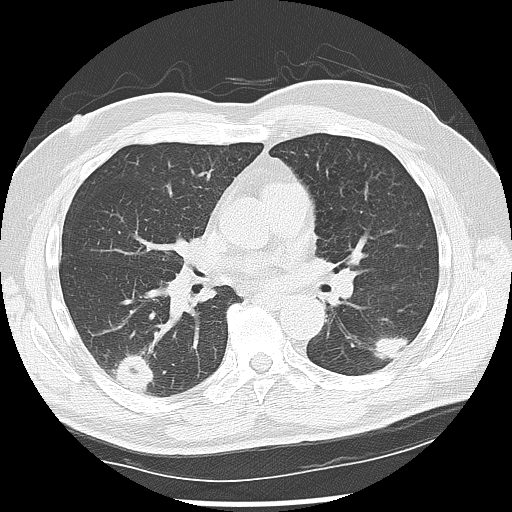
Low-dose screening chest CT, one axial slice; position 69 of 142 along the scan axis; reconstruction kernel LUNG; 120 kVp; lung window (W 1500 / L -600 HU); 2.5 mm slice thickness; 512 × 512 image matrix, field of view 360 × 360 mm.
Outlined on this slice (expert manual segmentation):
- lesion 1 (nodule, lower lobe of left lung): bounding box [x1, y1, x2, y2] px = [370, 336, 408, 362]
- lesion 2 (nodule, lower lobe of right lung): [113, 352, 154, 392]